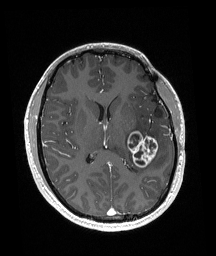
Brain MRI from a brain-tumour surgery series, one axial slice. Slice 83 of 192 in the series (ordered by position). T1-weighted post-contrast. 216 × 256 image matrix, field of view 211 × 250 mm. Case-level facts recorded for this patient, not image findings: histopathology: Glioneuronal tumor; WHO grade: 2; tumour location: Left Superior Temporal Gyrus.
Annotated regions visible in this slice (manually delineated by an expert):
- tumour: bounding box [x1, y1, x2, y2] px = [127, 131, 159, 168]